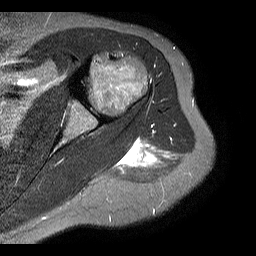
MRI of an extremity soft-tissue mass, one axial slice; position 12 of 20 along the scan axis; STIR; 4 mm slice thickness; 256 × 256 image matrix, field of view 150 × 150 mm. Female patient. From the clinical record (not read from this slice): histological type: malignant fibrous histiocytoma; grade: low; site of the primary tumour: left arm.
Structures marked on this image (expert manual segmentation):
- gross tumour volume (mass): bounding box <122,141,158,169> (left, top, right, bottom; pixels)